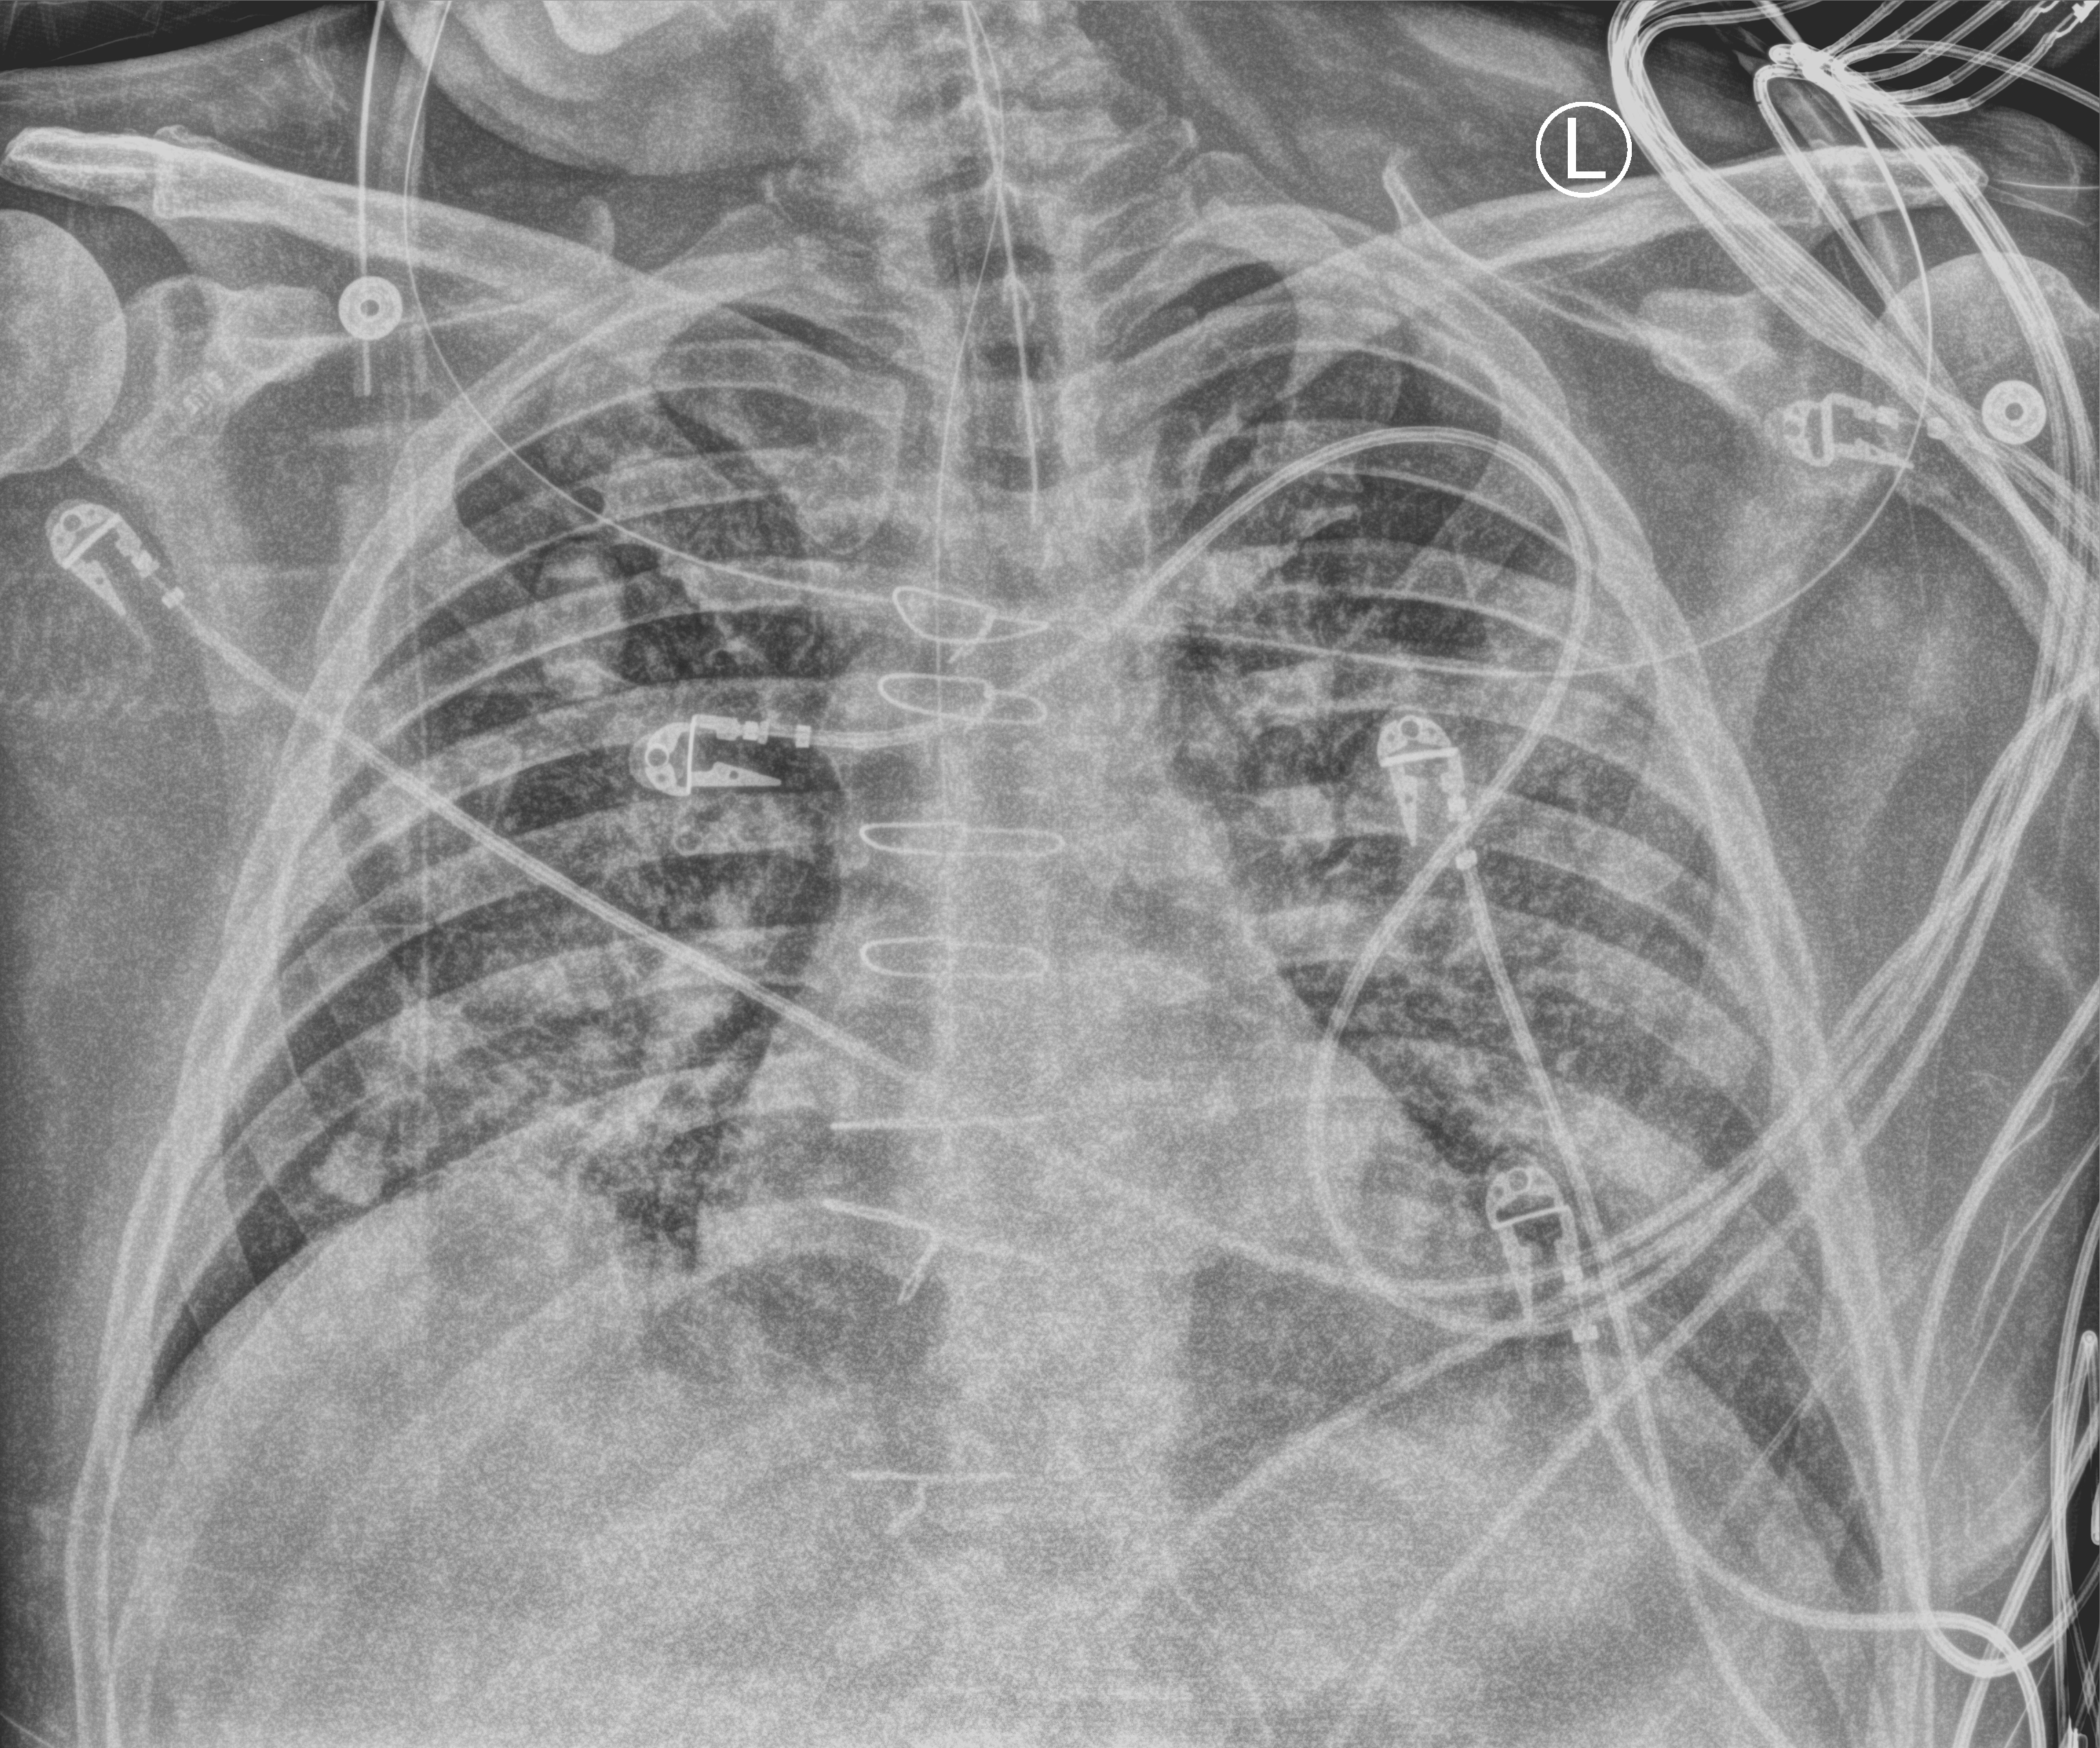
Bedside chest radiograph (computed radiography); anteroposterior (AP) projection. Male patient hospitalised with COVID-19, age 60–74 years.
Hospital-stay facts (about this admission, not read from this image; timing relative to this image not recorded):
- admitted to intensive care during this hospital stay: yes